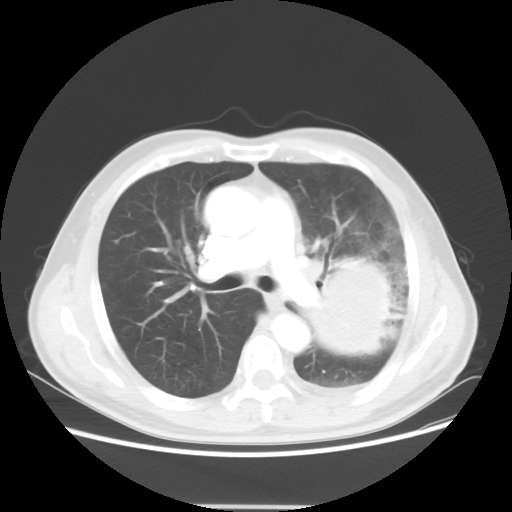
Chest CT, one axial slice; position 33 of 53 along the scan axis; reconstruction kernel STANDARD; lung window (W 1500 / L -600 HU); 512 × 512 image matrix. Patient: male, 60 years. Case-level facts recorded for this patient, not image findings: clinical TNM (as recorded): T4 N1 M1a; histopathological grade: G3.
Annotated regions visible in this slice (rectangle marked by the reading radiologist):
- lung tumour (recorded histology: large cell carcinoma): bounding box [x1, y1, x2, y2] px = [312, 251, 418, 374]